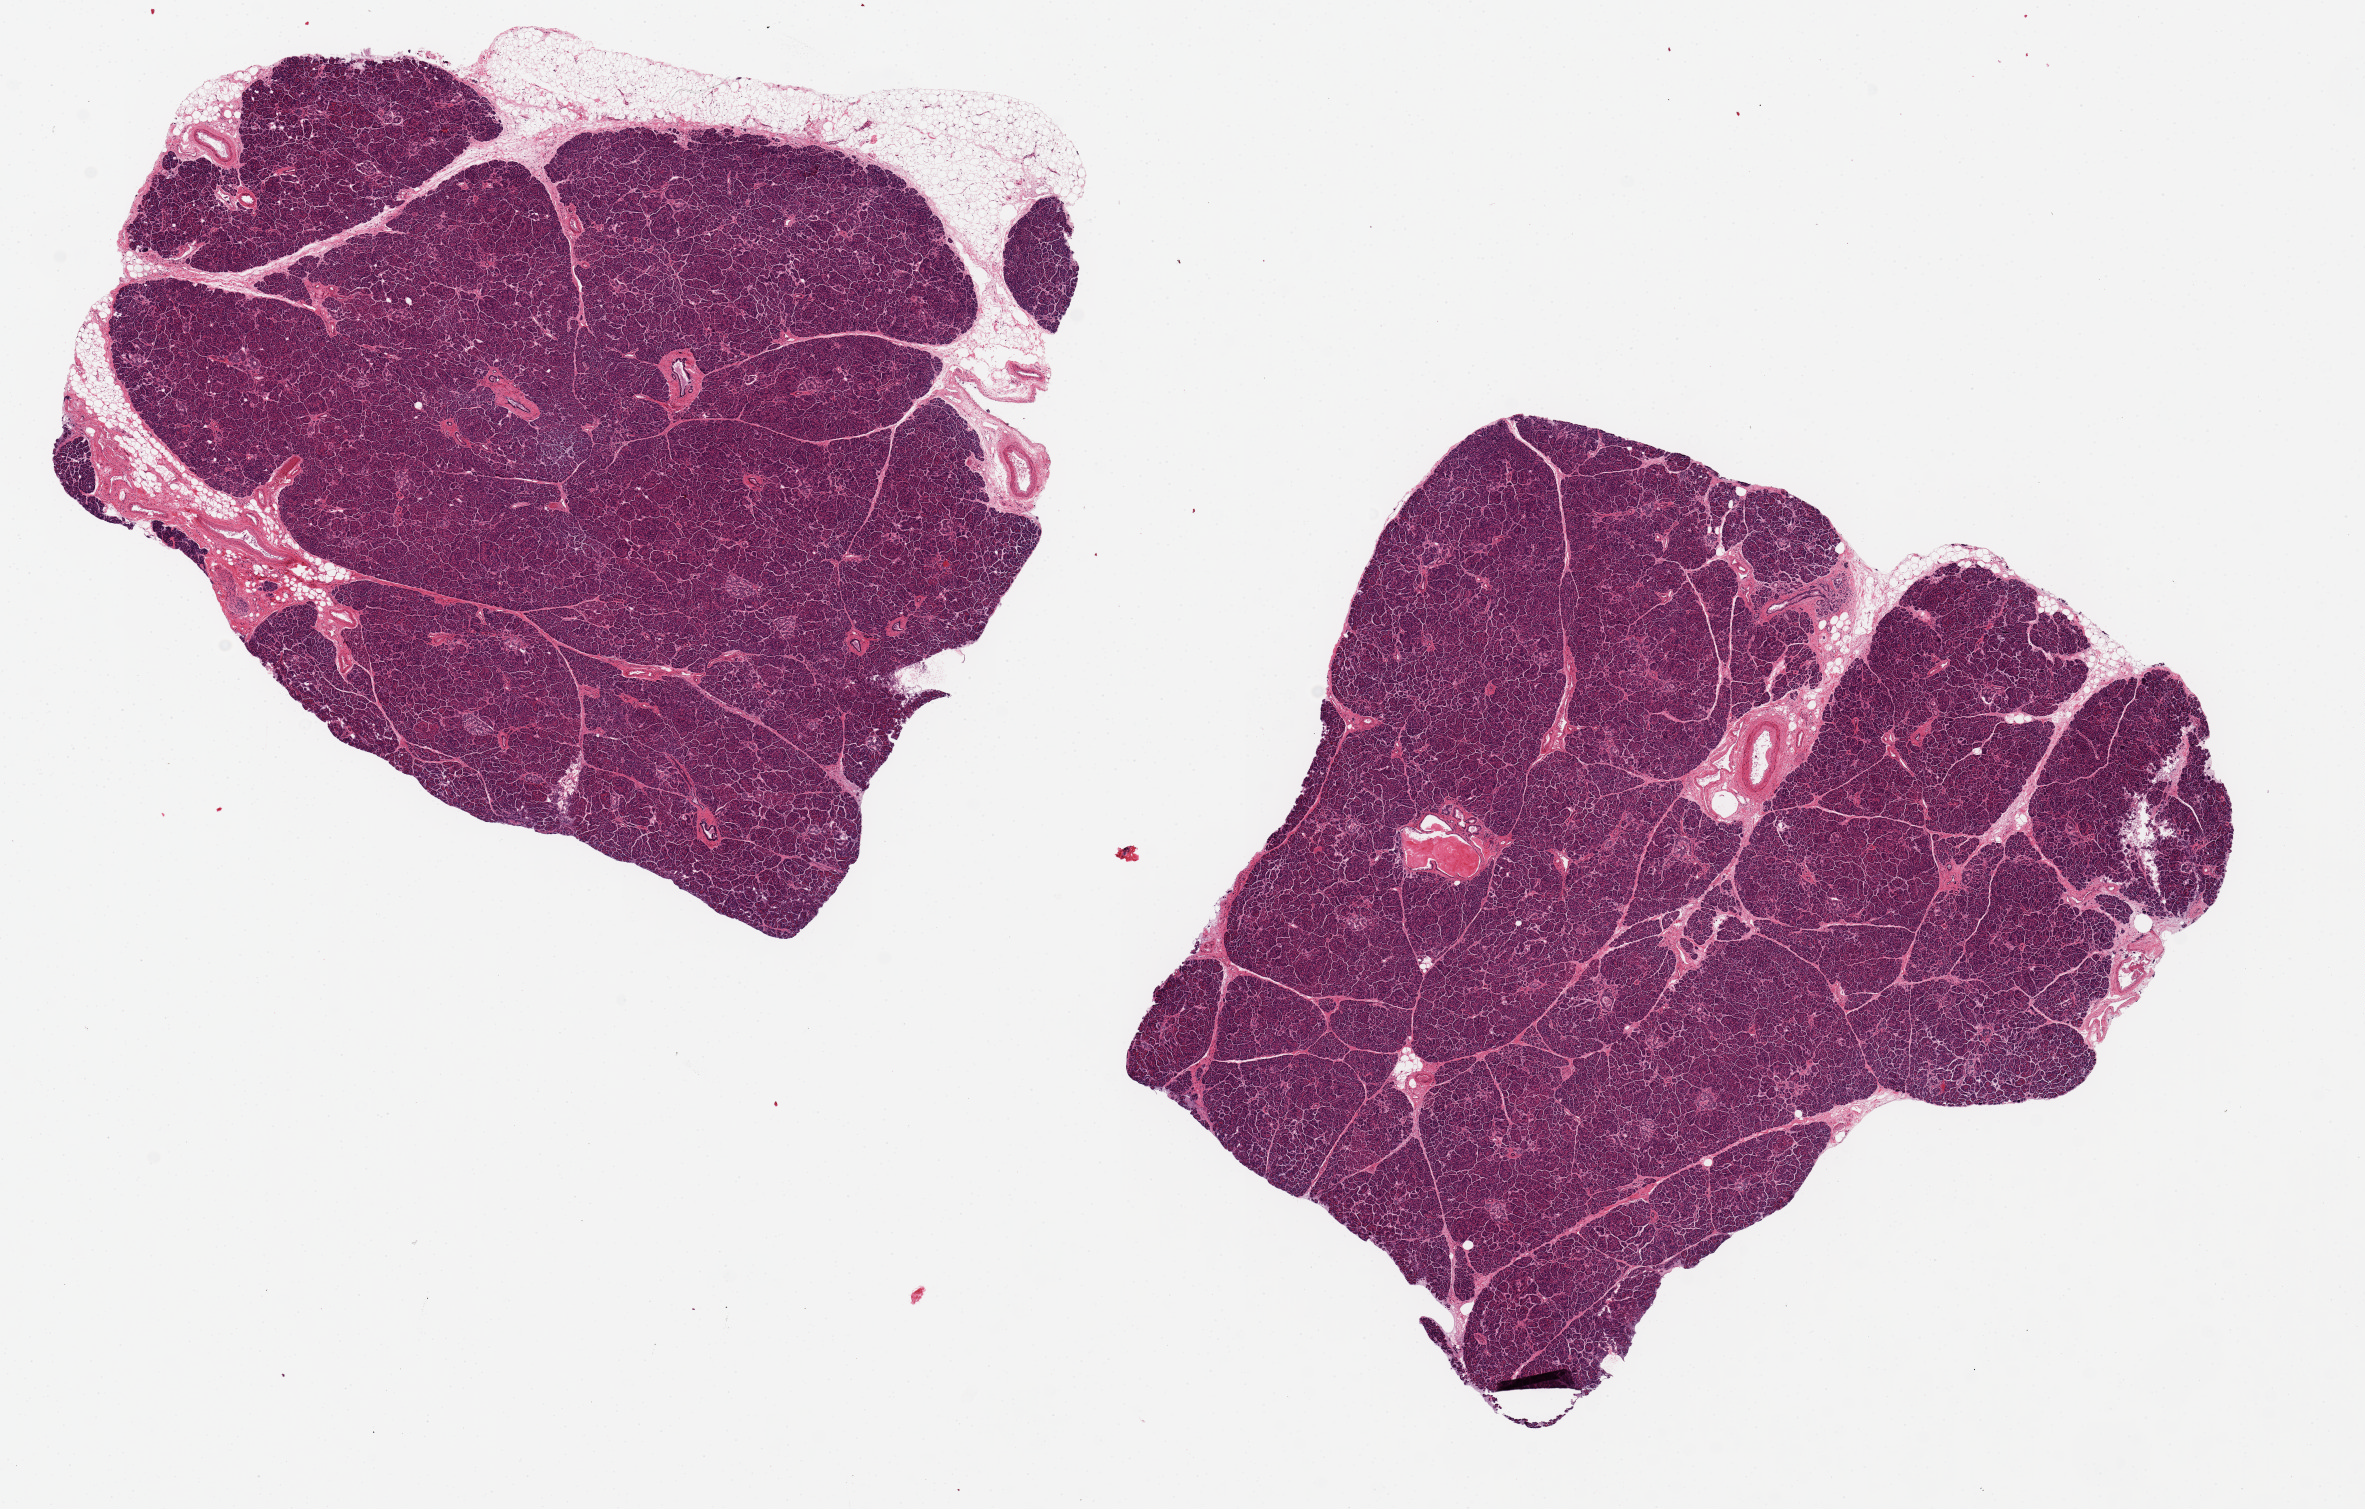
Whole-slide image, H&E stain — low-resolution overview of the scanned area, about 18.7 x 11.9 mm (acquisition: 20x scan); PAXgene-fixed paraffin-embedded (PFPE) section; target tissue: pancreas; donor tissue sample. Male donor.
• reviewer comment on this tissue sample: 2 ~7x6.5mm aliquots, remarkably well preserved no saponification. One aliquot with 5x0.5mm adherent fat; otherwise clean specimens